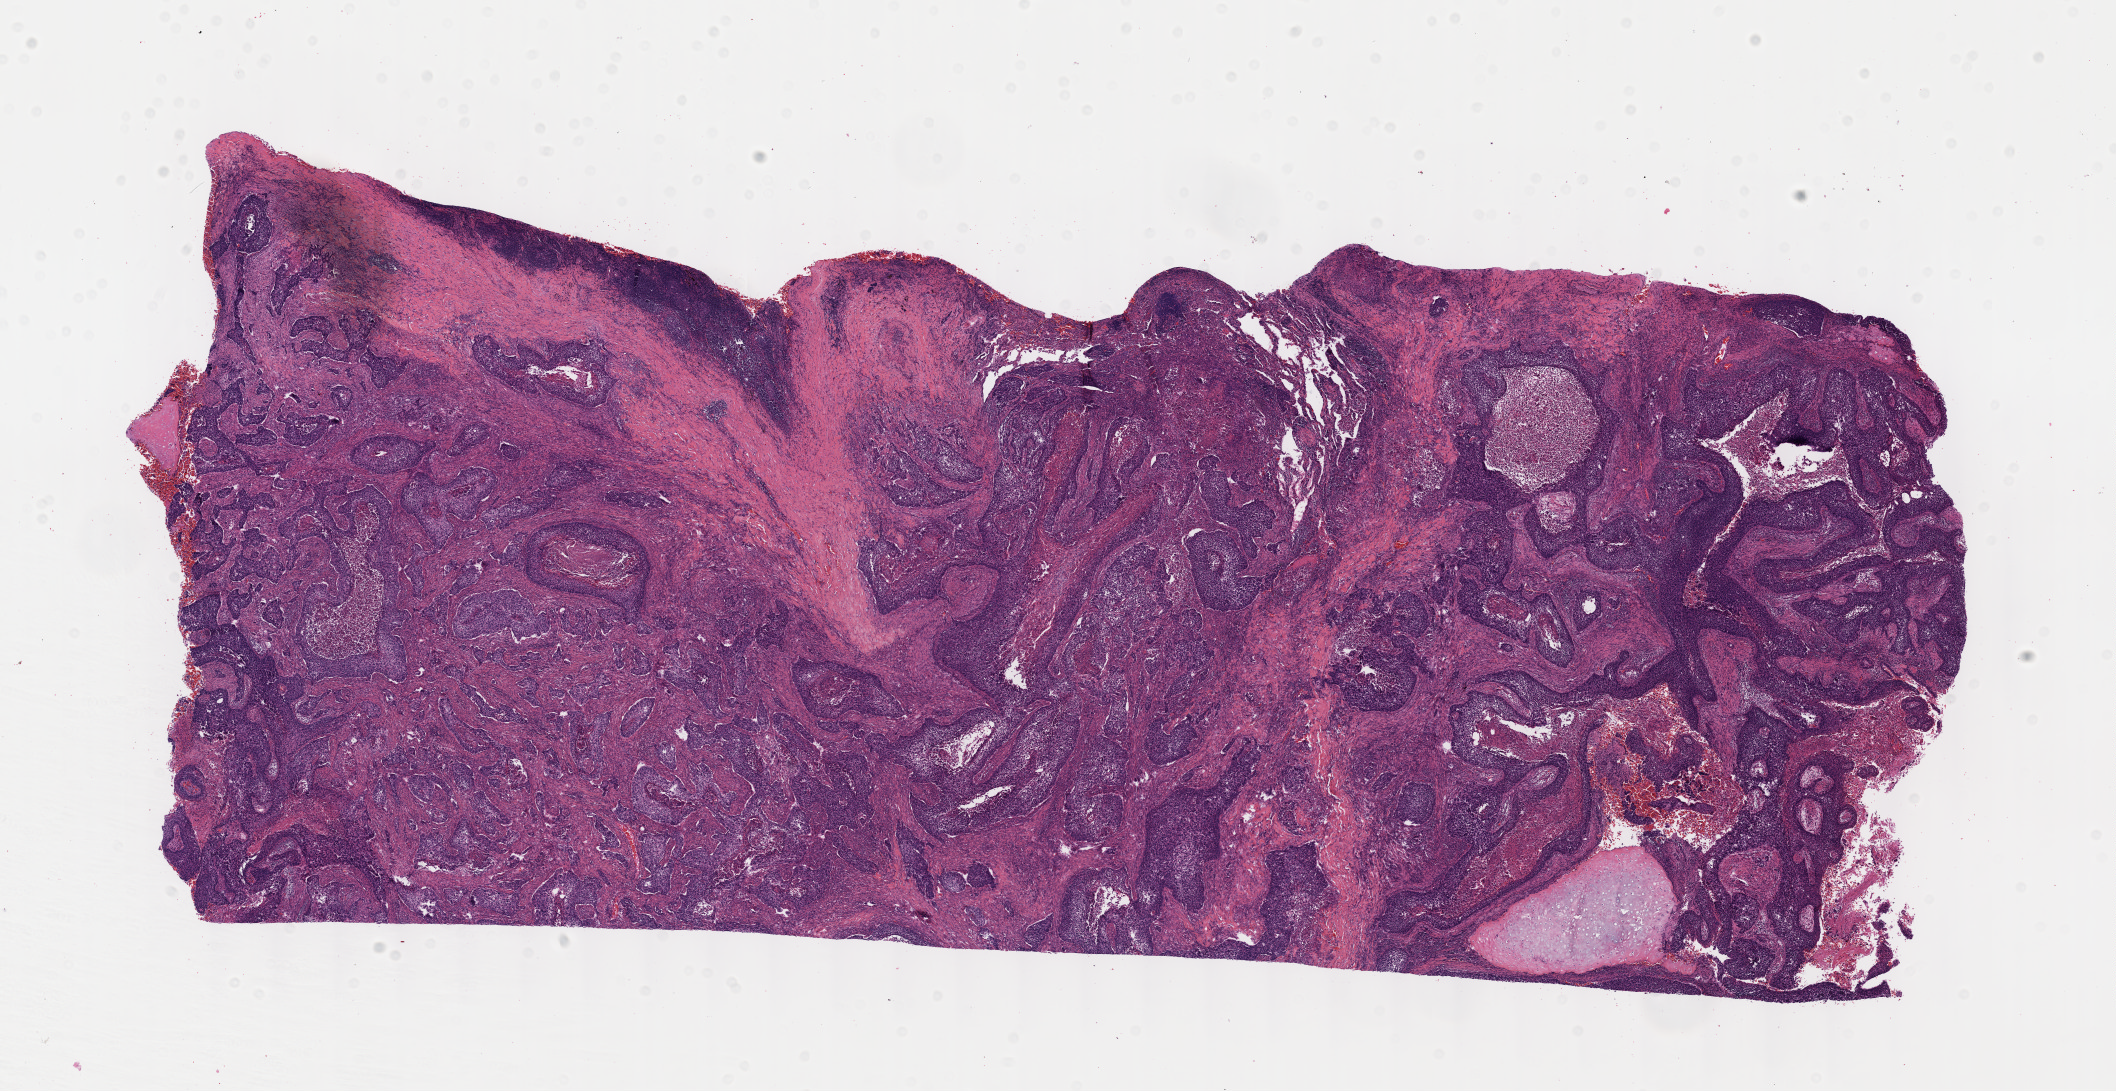
Whole-slide histology image, H&E — low-resolution overview of the scanned area, about 17.1 x 8.8 mm, formalin-fixed paraffin-embedded (FFPE) diagnostic section, sample: primary tumour, lung. Patient: male, age at initial diagnosis 49 years.
Laterality: left. Histologic diagnosis: Squamous cell carcinoma, NOS (upper lobe, lung). AJCC pathologic stage: II (7th edition).